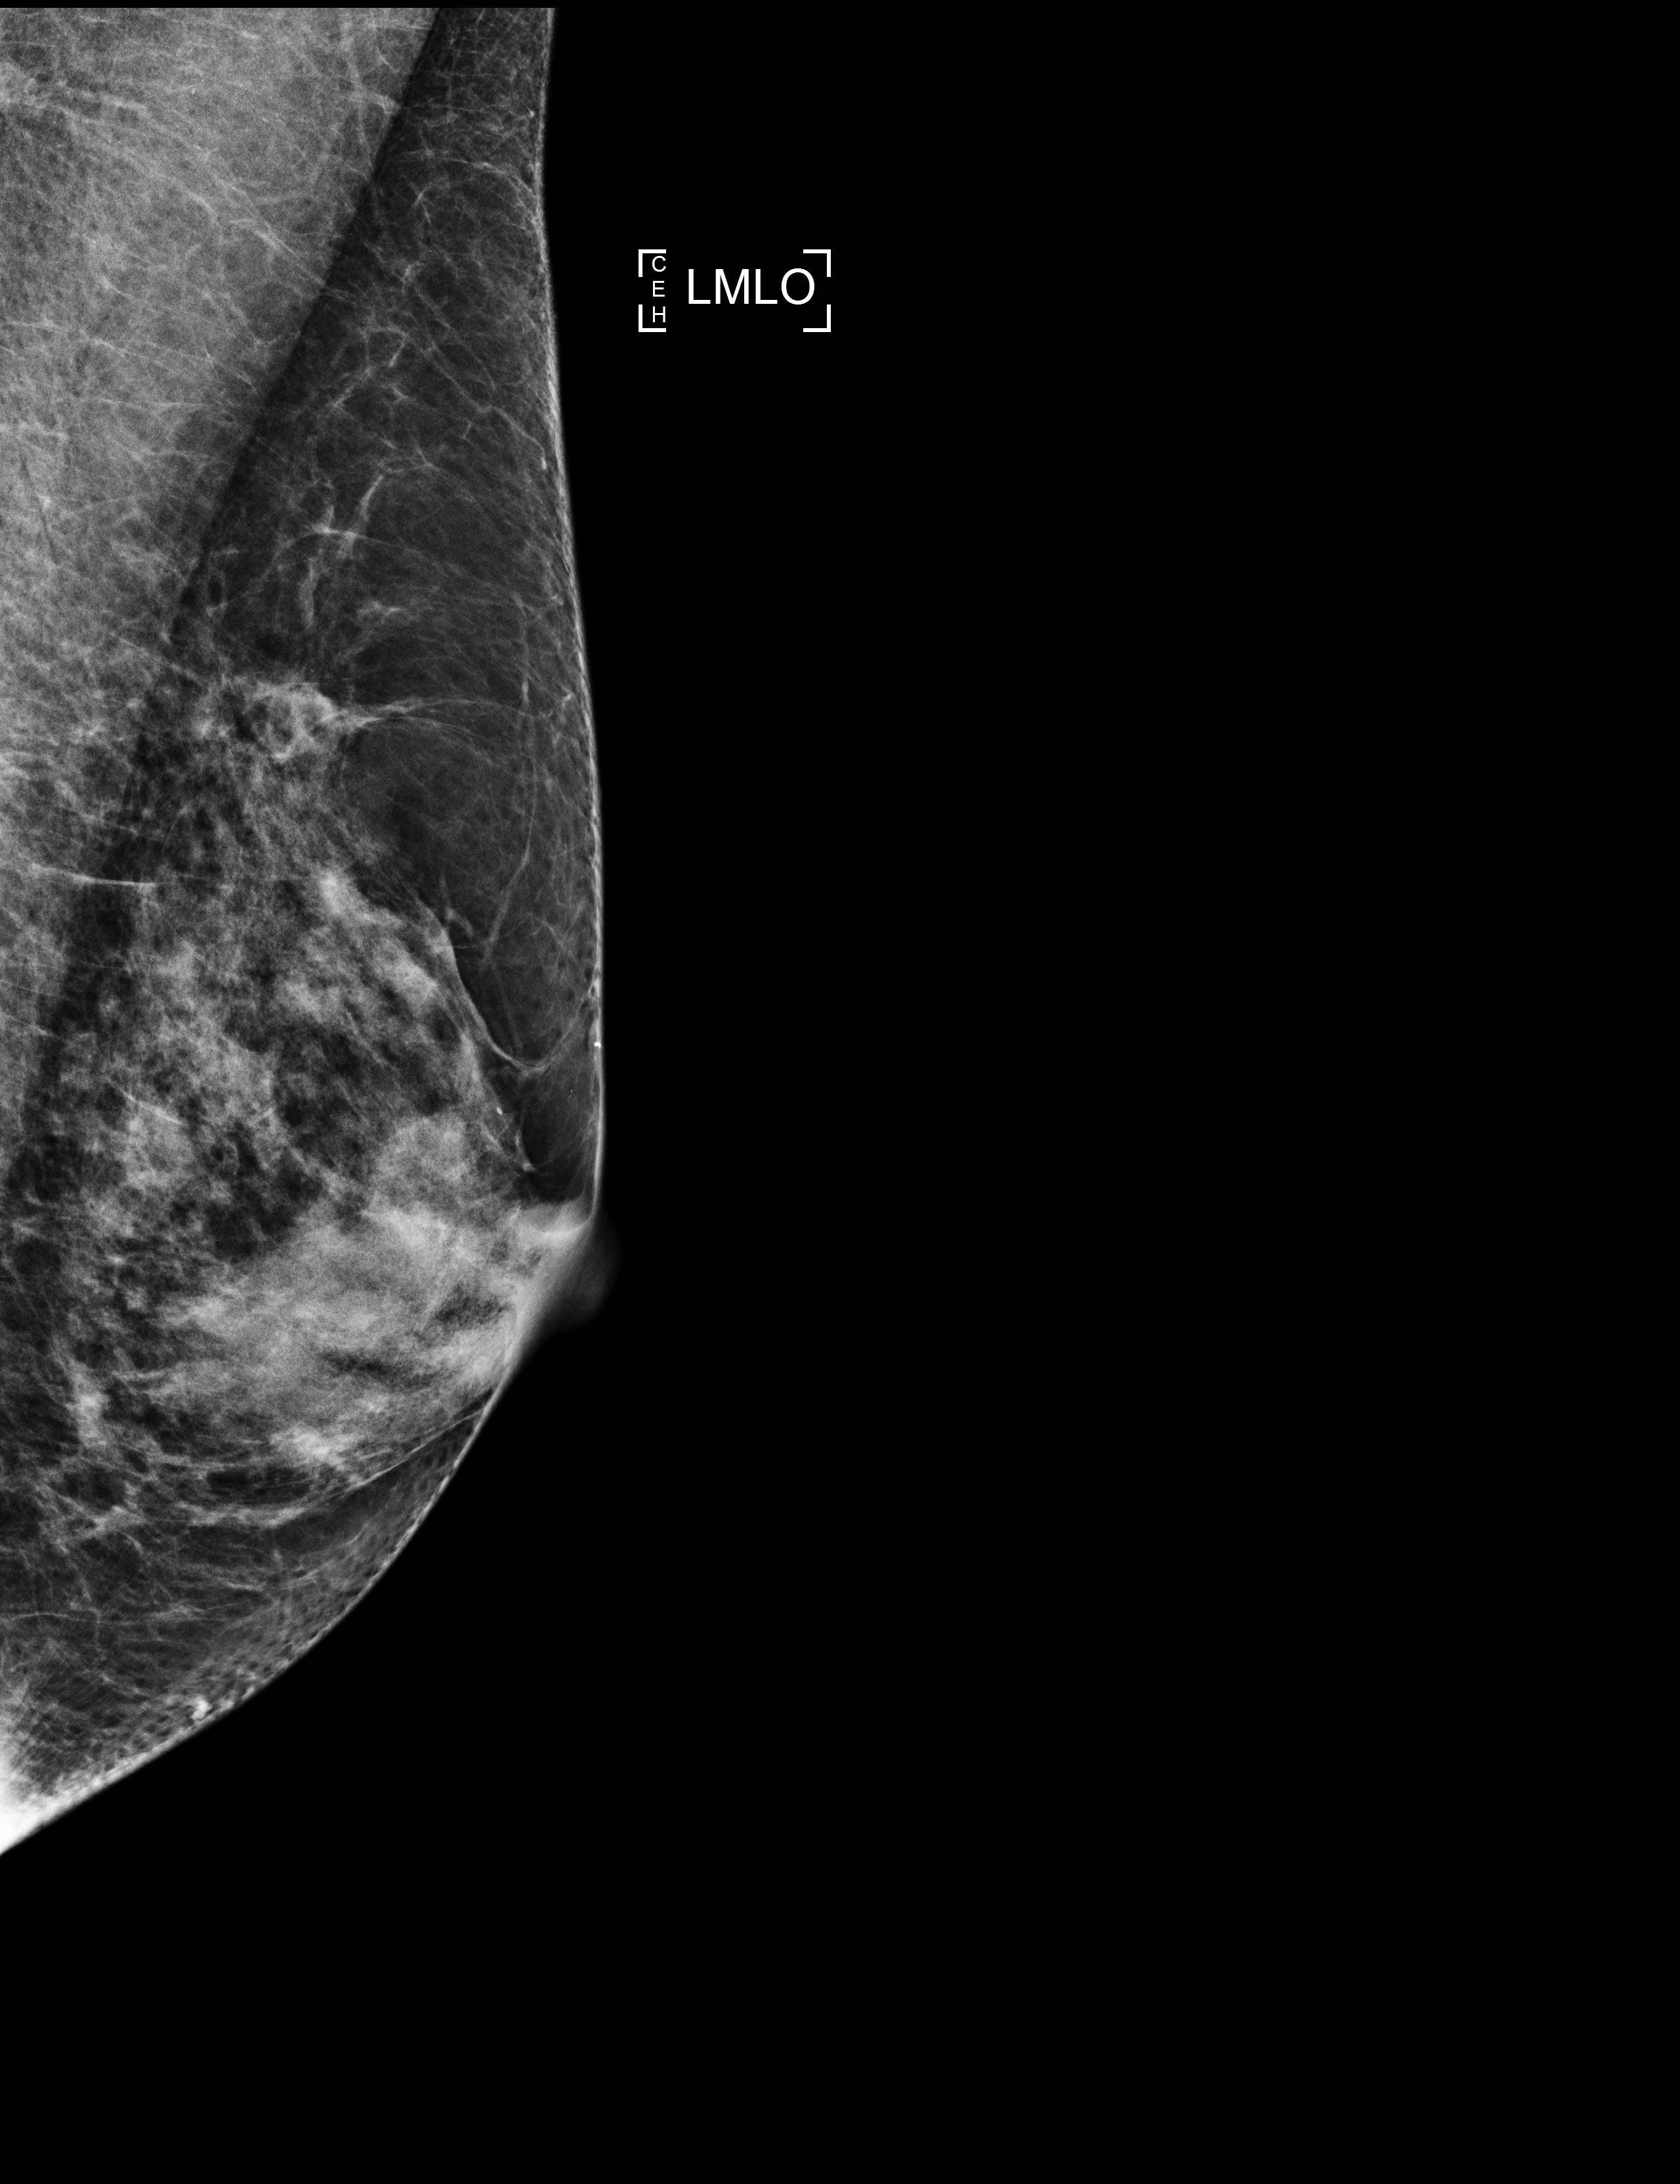
Annual screening mammography examination, system: Selenia Dimensions. Patient: female, 60 years.
Image type: full-field digital mammogram. Breast: left. Projection: mediolateral oblique (MLO) view.